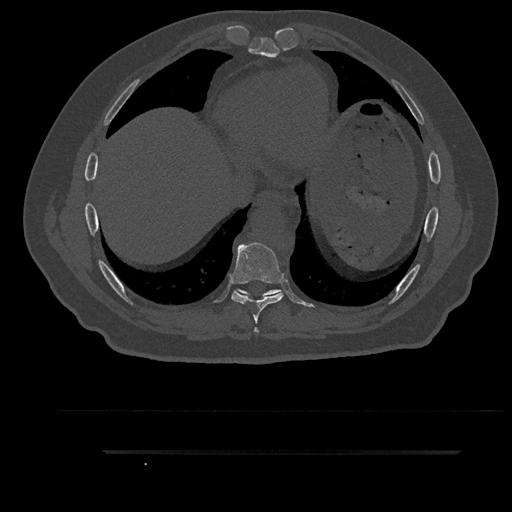
CT including the spine, one axial slice. Reconstruction kernel Br40s/3. 120 kVp. Bone window (W 1800 / L 400 HU). 0.5 mm slice thickness. 512 × 512 image matrix, field of view 432 × 432 mm. Male patient, age 63 years. Case-level facts recorded for this patient, not image findings: primary cancer: renal; vertebrae with lytic lesions (as recorded): T8.
Structures marked on this image (semi-automatic segmentation, software-assisted and operator-edited):
- T7 vertebra: bounding box <254,328,259,333> (left, top, right, bottom; pixels)
- T8 vertebra: <231,242,284,324>
- T9 vertebra: <236,289,281,299>